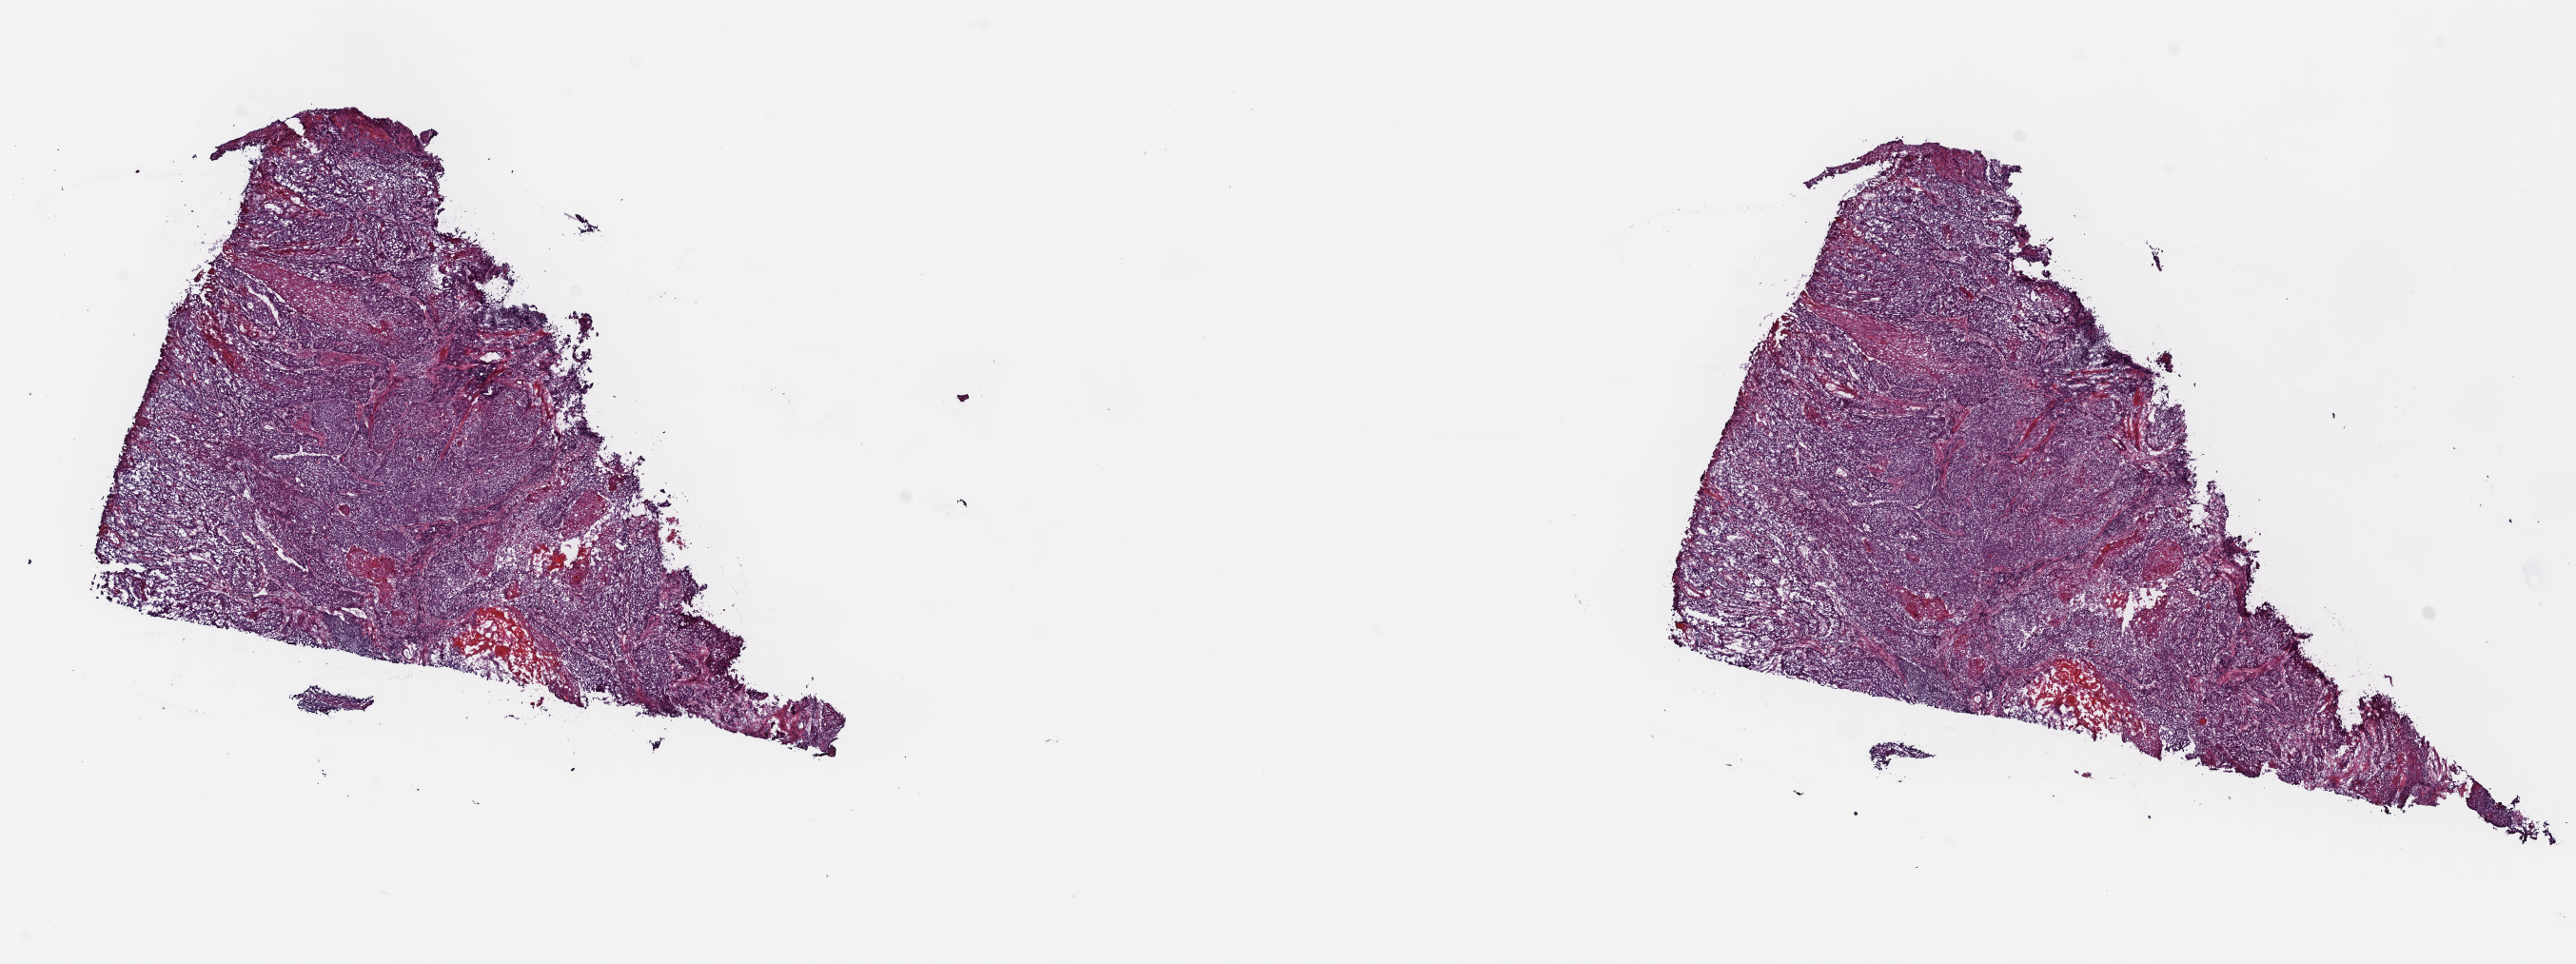
Digitized Hematoxylin and eosin (H&E) stained tissue section (whole slide) — low-resolution overview of the scanned area, about 21.3 x 8.0 mm (slide scanned at 40x), frozen section from the top of the tissue portion, sample: primary tumour, esophagus. Patient: male, age at initial diagnosis 63 years. Histologic grade: G2 (moderately differentiated). Composition of this section per pathologist review: tumour cells 100%, tumour nuclei 80%, normal cells 0%, stromal cells 0%, necrosis 0%. Infiltration values recorded for this section: lymphocyte infiltration 0%, monocyte infiltration 0%, neutrophil infiltration 0%.
AJCC pathologic stage: IIB. Diagnosis: Squamous cell carcinoma, NOS (upper third of esophagus).